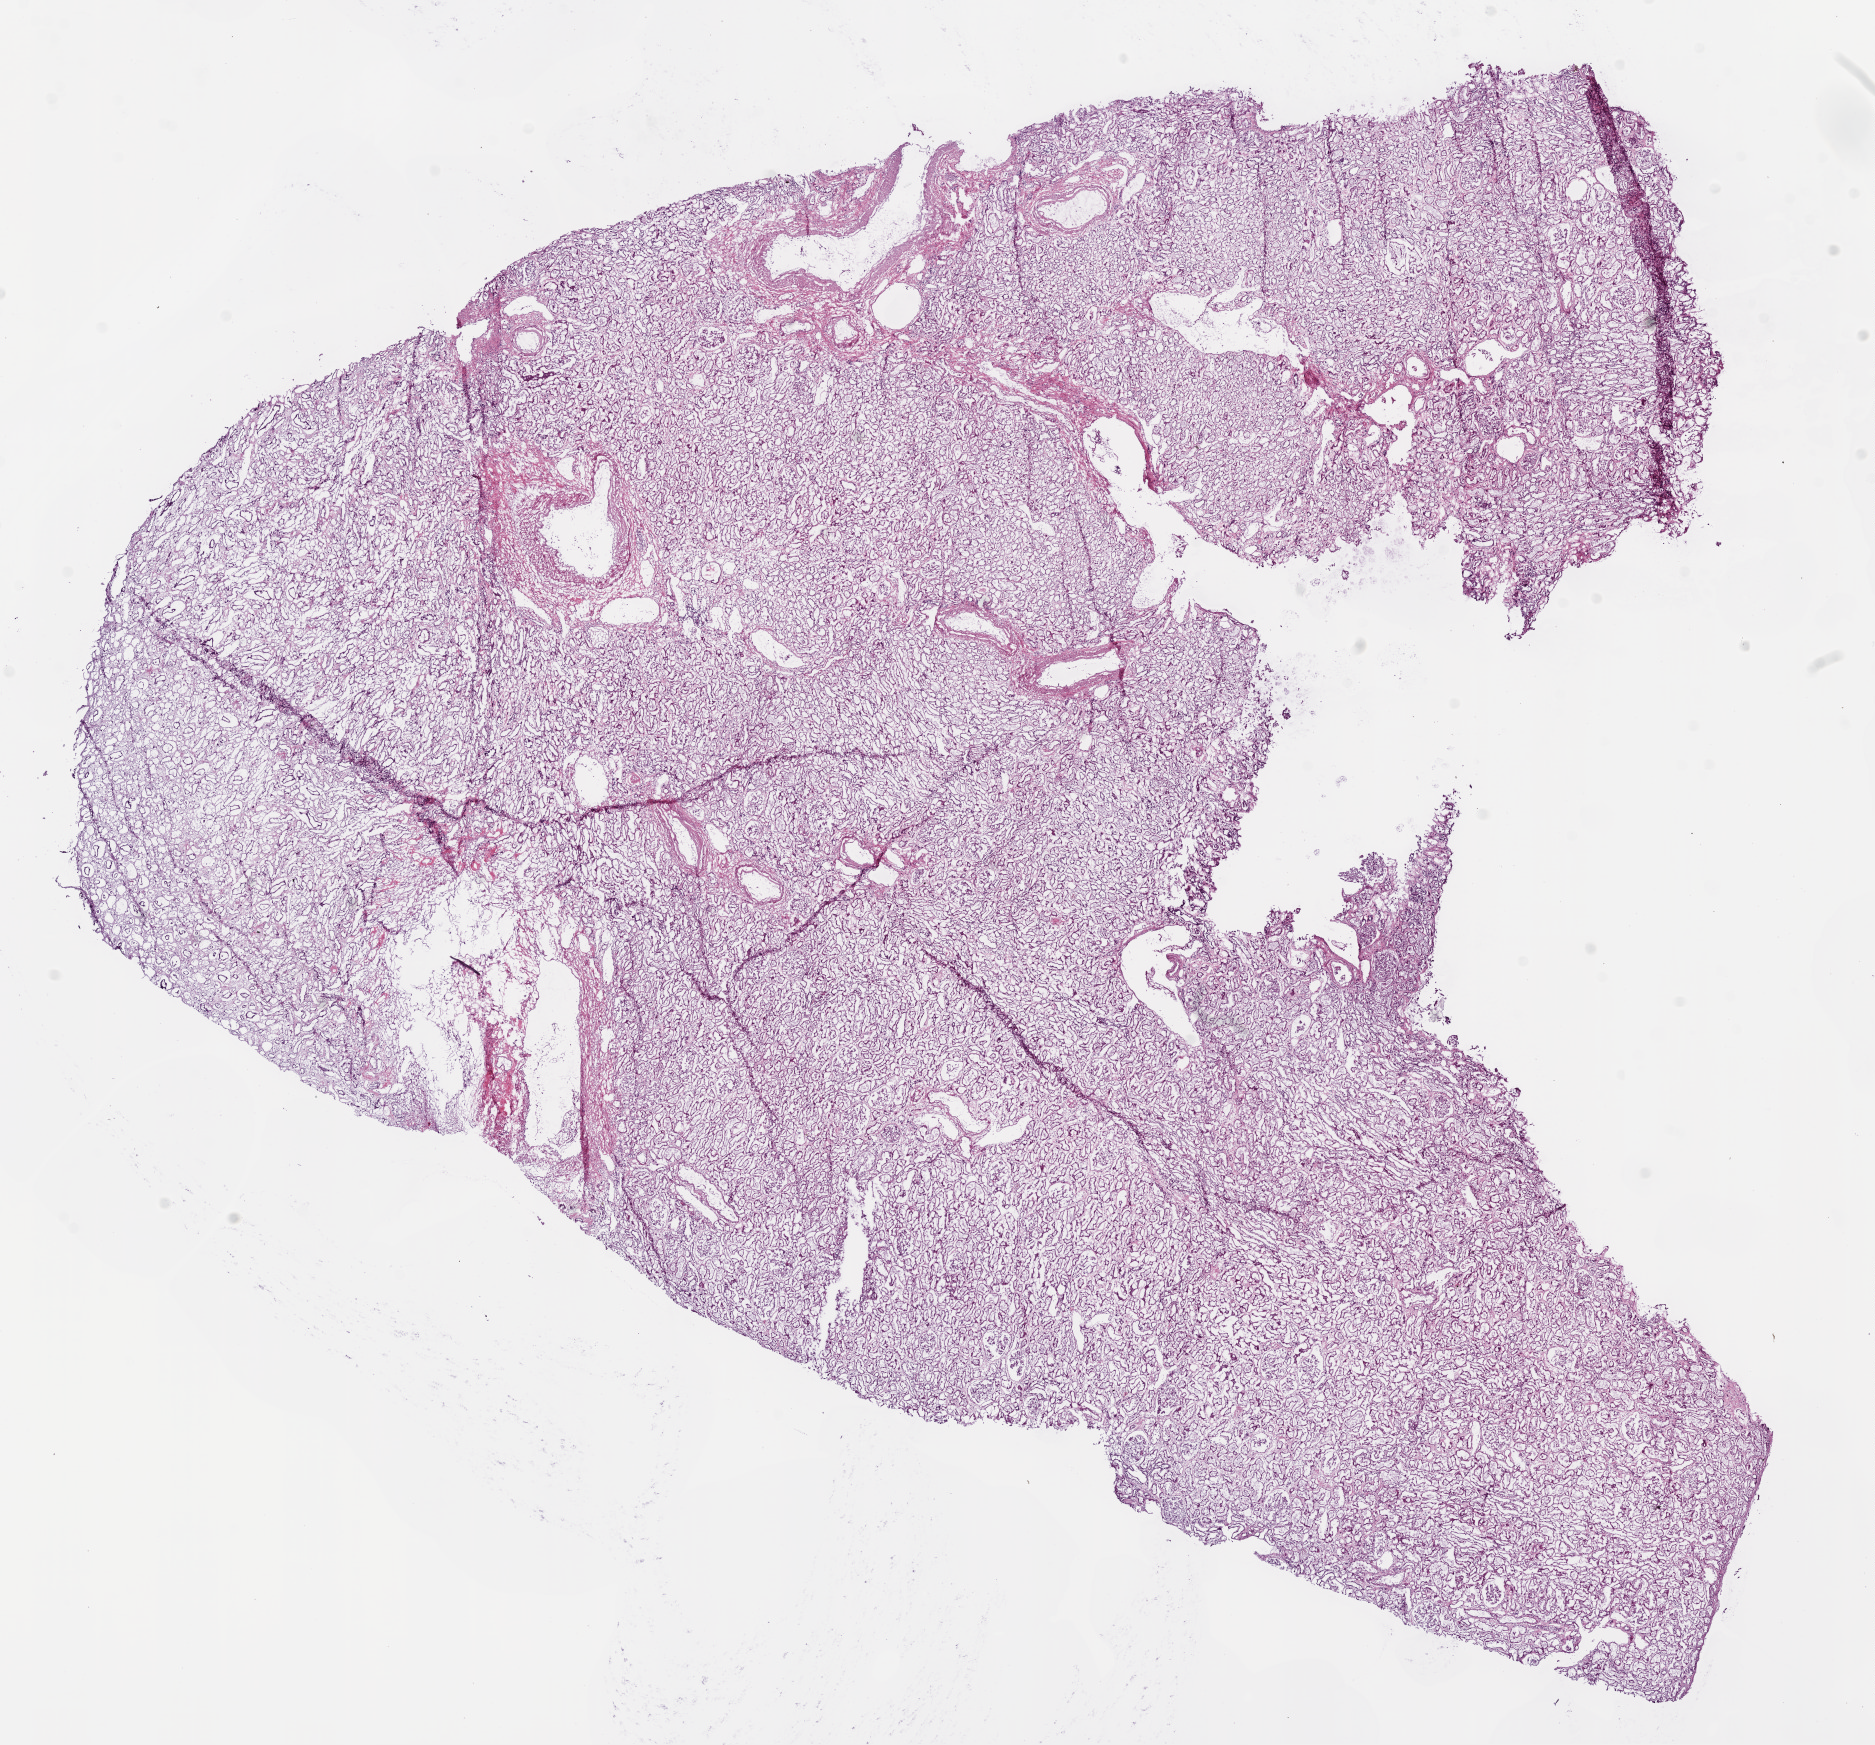
Digitized H&E-stained tissue section (whole slide) — shown as a low-resolution overview of the whole scanned area (about 15.0 x 14.0 mm, from a 20x scan); frozen section from the bottom of the tissue portion; solid tissue normal (non-tumour tissue) sample from the kidney. Female patient; age at initial diagnosis 51 years.
This section: solid tissue normal (non-tumour) sample from the same patient. Patient diagnosis: Clear cell adenocarcinoma, NOS.